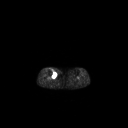
FDG PET of an extremity soft-tissue mass (from a PET/CT study), one axial slice. Slice 146 of 267 in the series (ordered by position). 3.27 mm slice thickness. 128 × 128 image matrix. Female patient, age 65 years. From the clinical record (not read from this slice): histological type: undifferentiated – high grade; grade: high; site of the primary tumour: right thigh.
Structures marked on this image (expert contour drawn on MRI and transferred to this co-registered scan by the dataset authors):
- gross tumour volume (mass): bounding box [x1, y1, x2, y2] px = [51, 70, 57, 78]